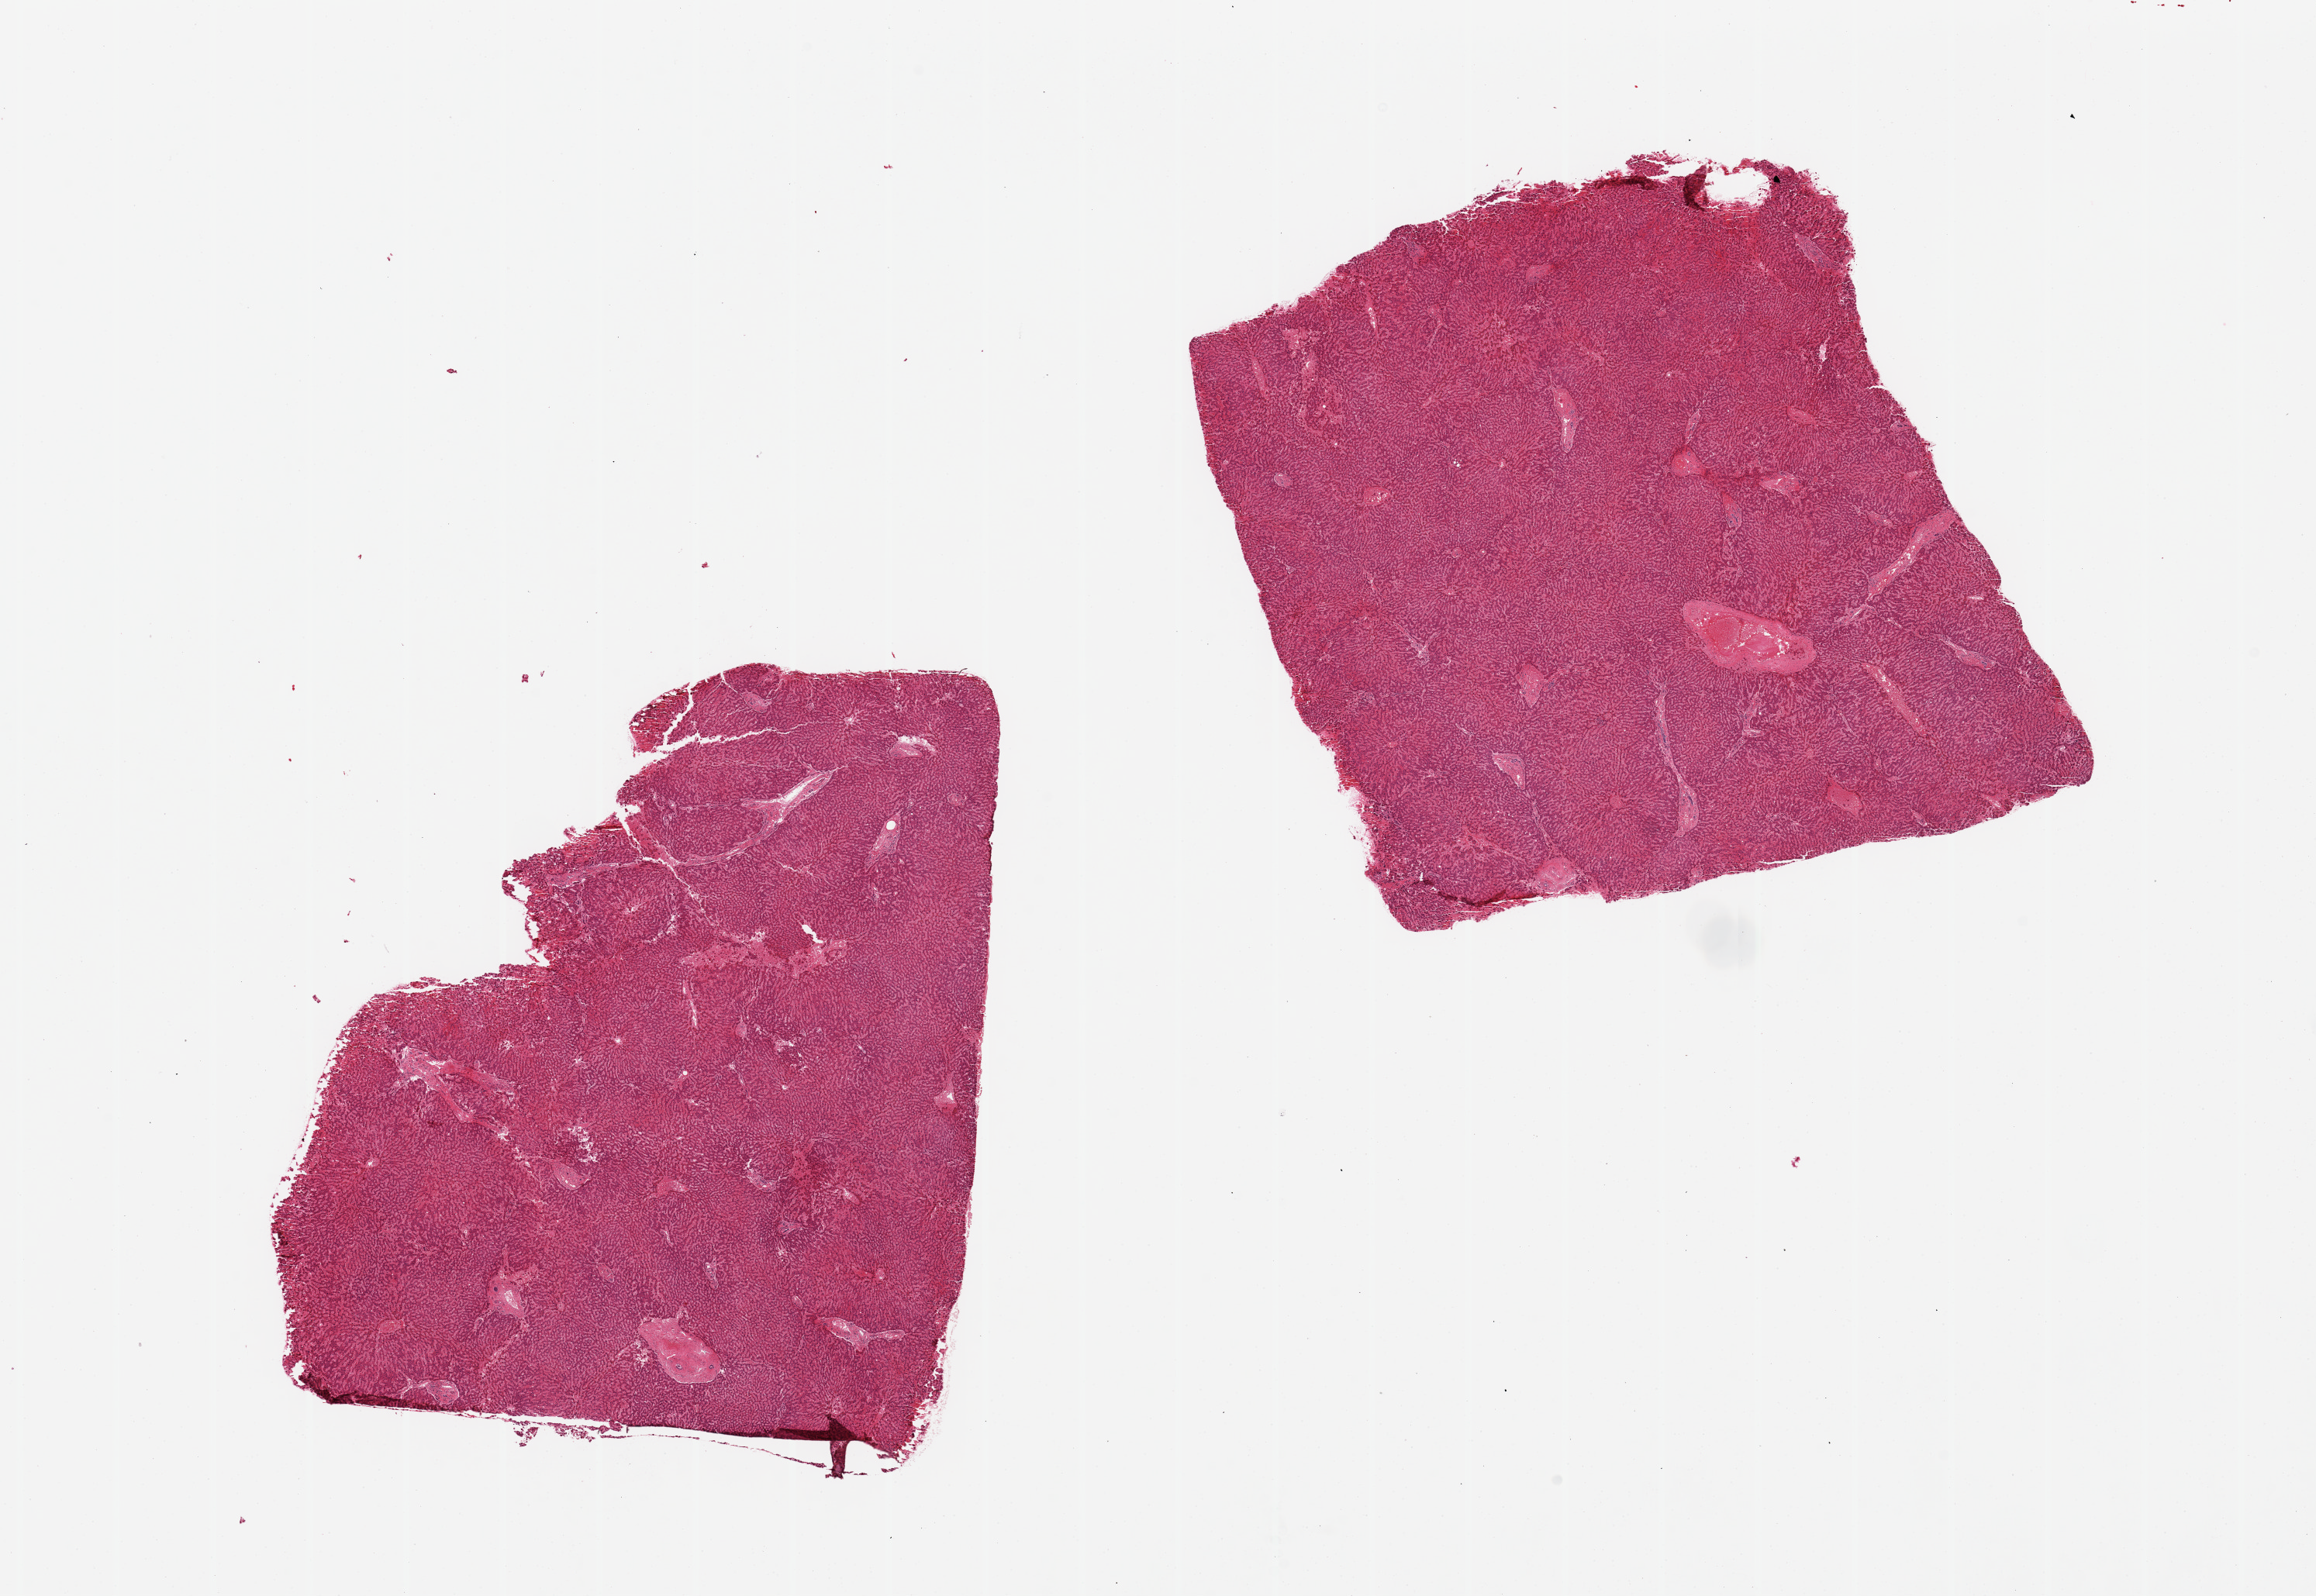
Digitized hematoxylin and eosin (H&E)-stained section — shown as a low-resolution overview of the whole scanned area (about 23.6 x 16.3 mm, acquisition: 20x scan), PAXgene-fixed, paraffin-embedded tissue, section of liver (target tissue), donor tissue sample.
* pathologist's review note for this sample: 2 pieces; no fat or inflammation